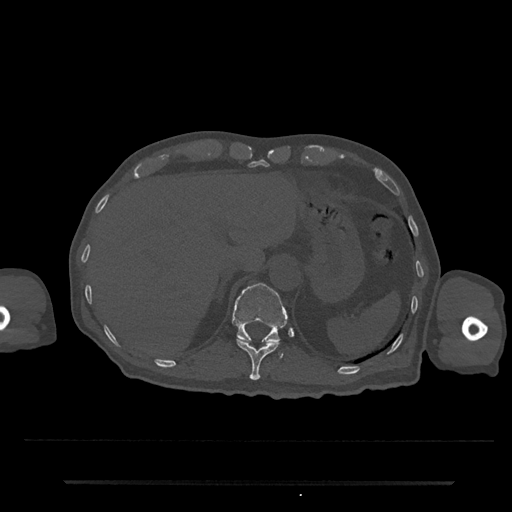
CT including the spine, one axial slice; slice 228 of 797 in the series (ordered by position); 120 kVp; bone window (W 1800 / L 400 HU); 0.5 mm slice thickness; 512 × 512 image matrix. Patient: male, 74 years. Case-level facts recorded for this patient, not image findings: primary cancer: prostate.
Outlined on this slice (semi-automatic segmentation, software-assisted and operator-edited):
- T11 vertebra: bounding box (x1, y1, x2, y2) in pixels: (236, 339, 280, 380)
- T12 vertebra: (232, 283, 288, 357)